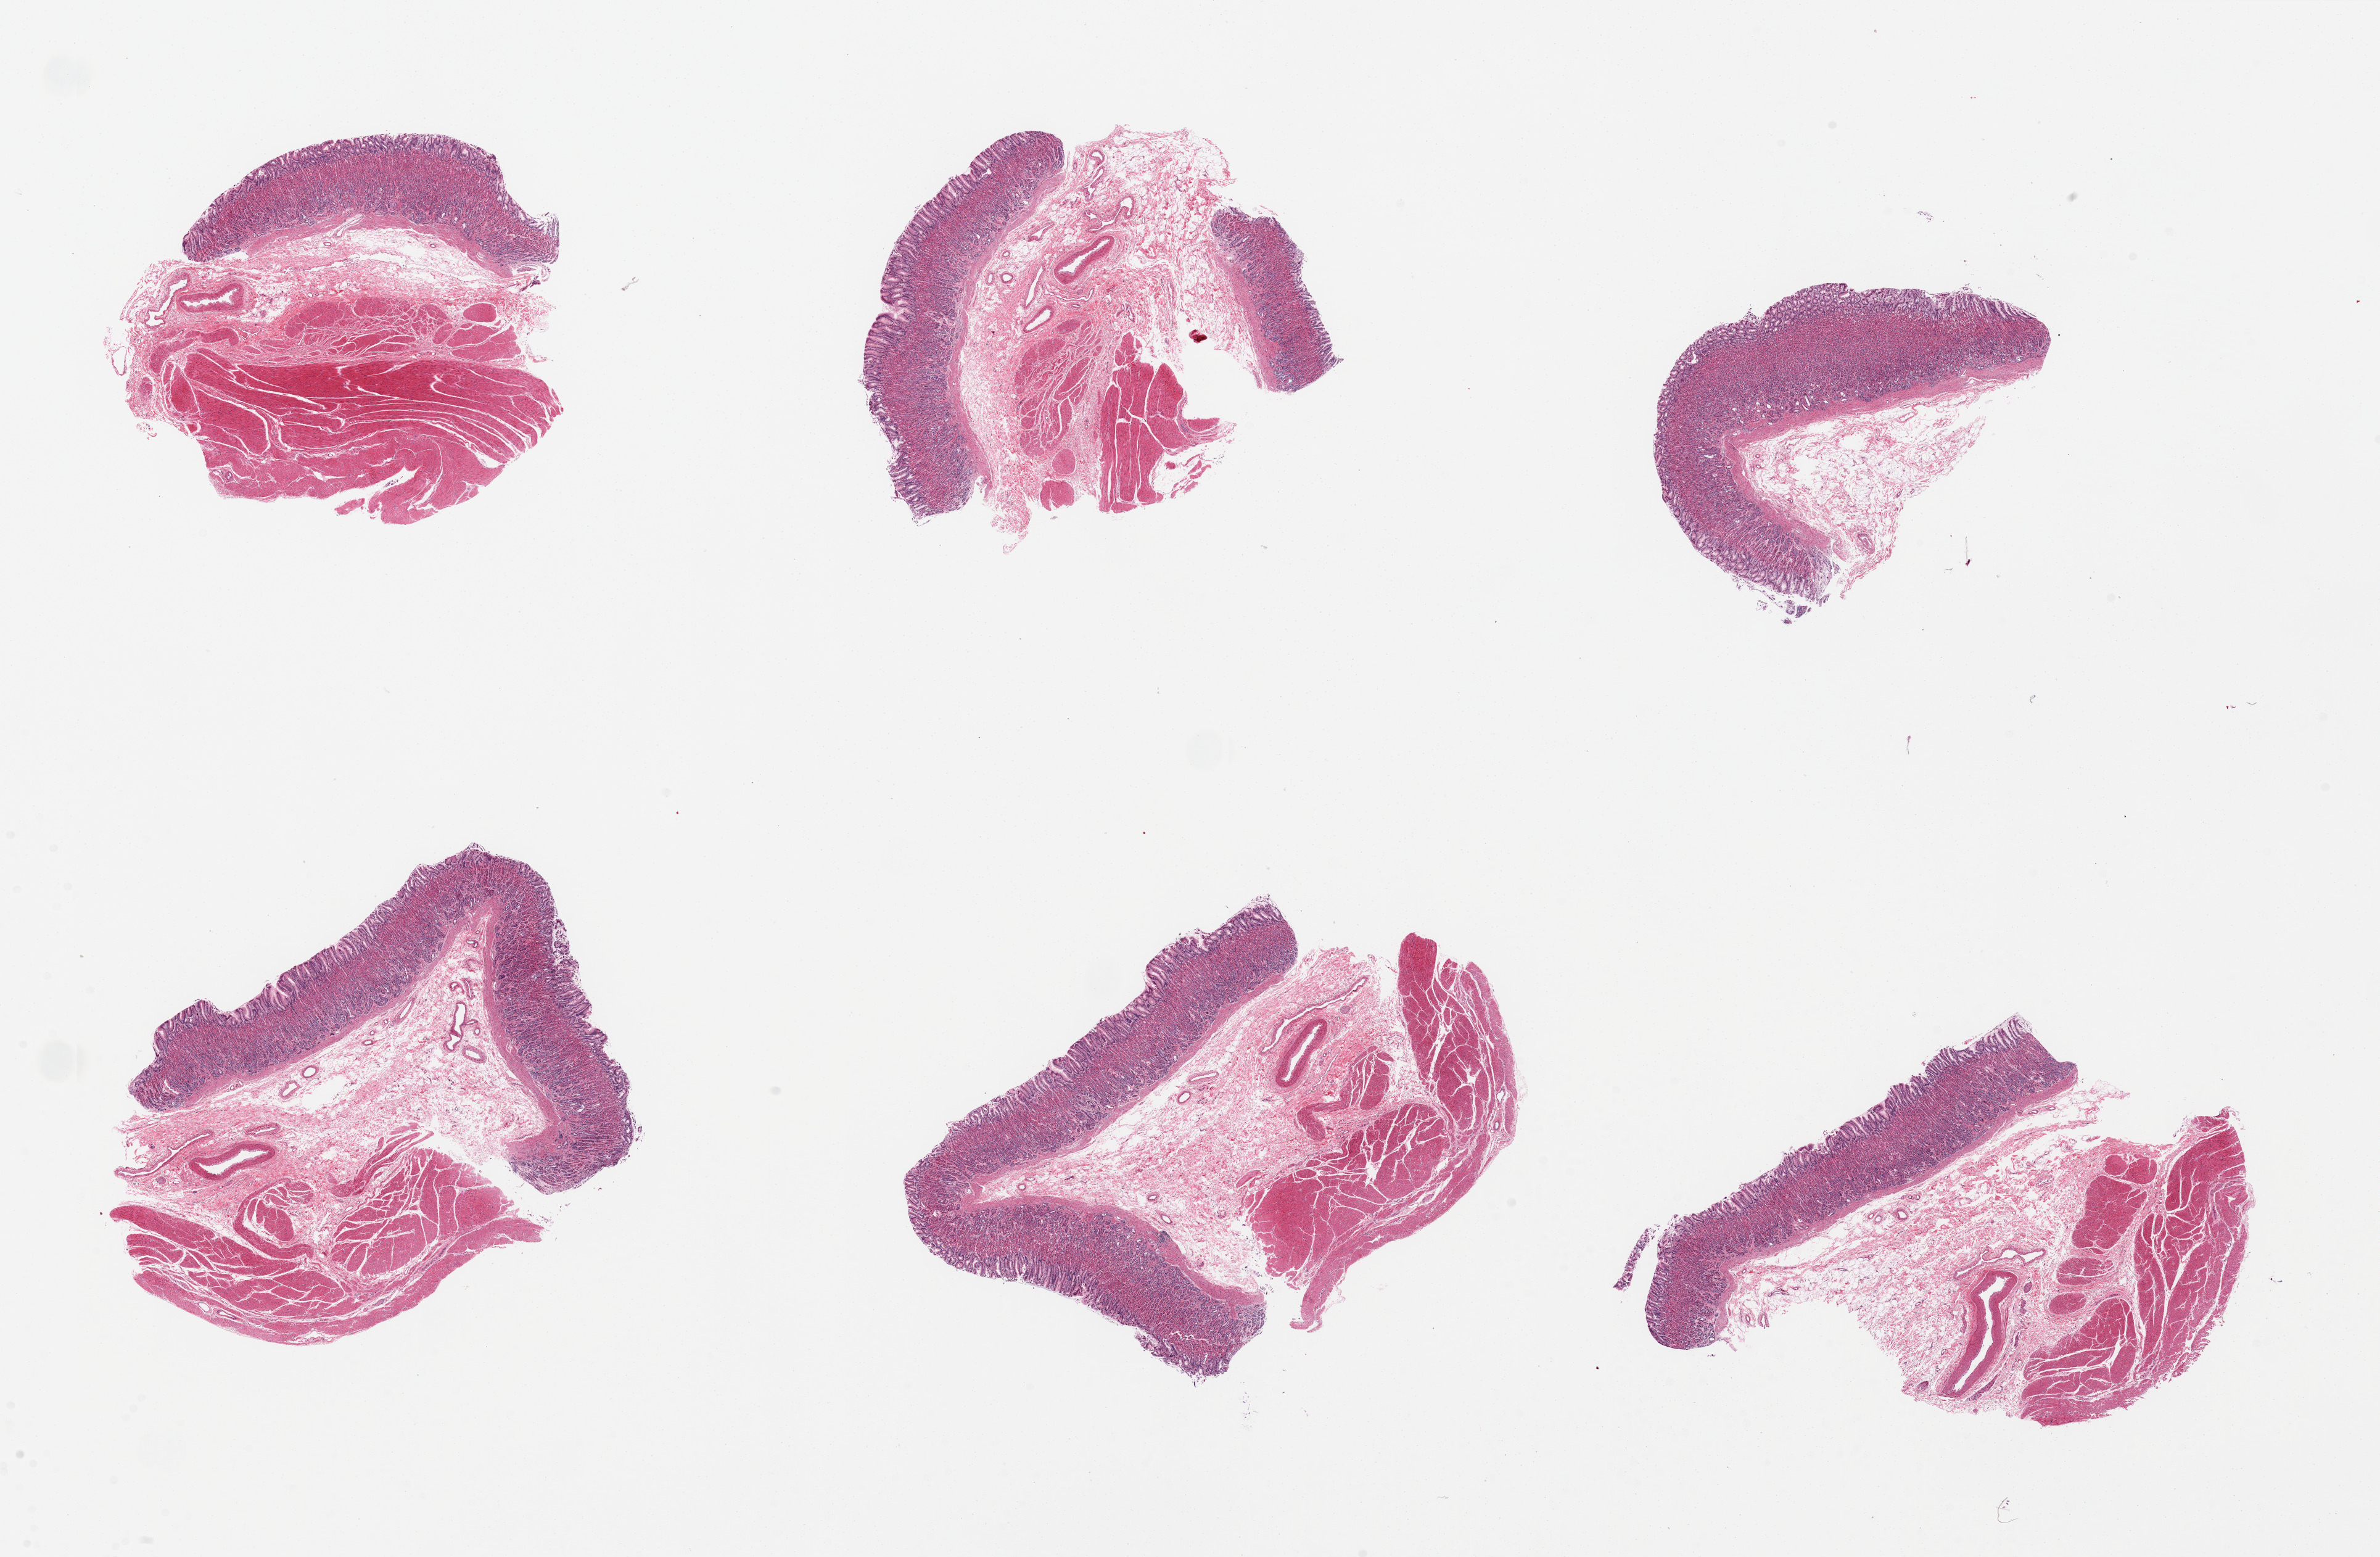
Whole-slide image, haematoxylin and eosin stain, brightfield, a low-resolution overview of the entire scanned area, about 30.5 x 20.0 mm (slide scanned at 20x). PAXgene-fixed, paraffin-embedded tissue. Section of stomach (target tissue). Tissue donor sample. Donor: female.
Pathologist's review note for this sample: 6 pieces, 5 with mucosa and muscularis, 1 mucosa only.